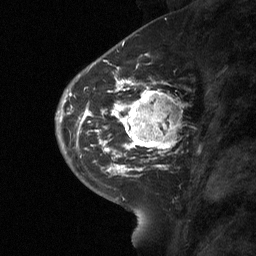
Breast MRI (dynamic contrast-enhanced), one sagittal slice. Slice 25 of 64 in the series (ordered by position). Dynamic contrast-enhanced study with each time point stored as its own series, time point 2 of 3 at this slice position (early post-contrast, ordered by acquisition time). 1.5 T. TE 4.8 ms, TR 27 ms. 2 mm slice thickness. 256 × 256 image matrix, field of view 180 × 180 mm. Female patient, age 42 years. From the clinical record (not read from this slice): setting: breast cancer imaged before/during neoadjuvant chemotherapy; receptor status: triple-negative.
Annotated regions visible in this slice (semi-automatic segmentation, software-assisted and operator-edited):
- analysis volume of interest (the breast-tissue region the enhancement analysis was run in; not a lesion): bounding box (x1, y1, x2, y2) in pixels: (115, 85, 180, 160)
- tumour enhancement mask (voxels above the 90 % enhancement threshold inside the analysis volume of interest): (115, 85, 177, 159)